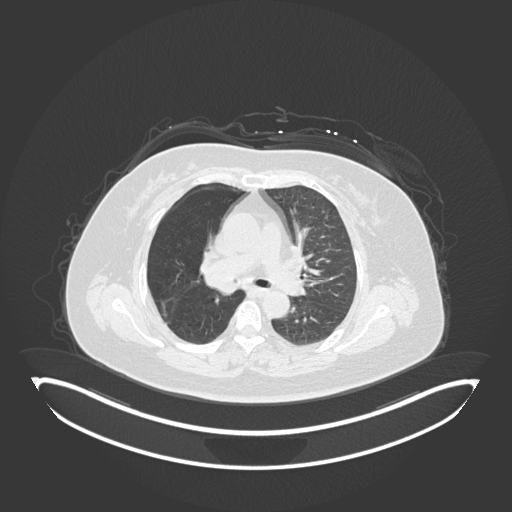
Chest CT, one axial slice; position 104 of 245 along the scan axis; reconstruction kernel B30f; lung window (W 1500 / L -600 HU); 1 mm slice thickness; 512 × 512 image matrix, field of view 500 × 500 mm. Patient: female, 60 years. Case-level facts recorded for this patient, not image findings: clinical TNM (as recorded): T1c N0 M0; histopathological grade: G1-G2.
Structures marked on this image (bounding box drawn by a radiologist):
- lung tumour (recorded histology: squamous cell carcinoma): bounding box [x1, y1, x2, y2] px = [198, 261, 244, 296]